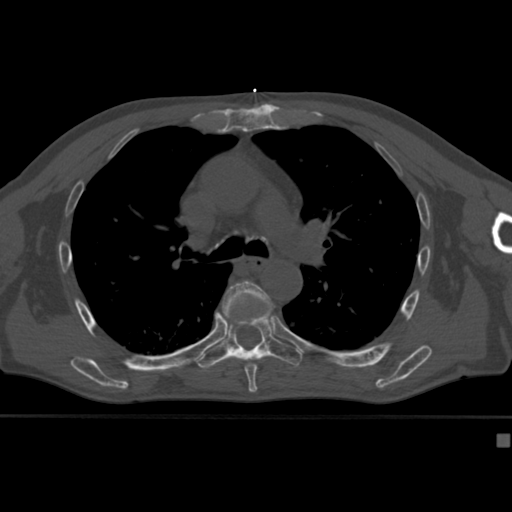
CT including the spine, one axial slice; slice 286 of 430 in the series (ordered by position); bone window (W 1800 / L 400 HU); 512 × 512 image matrix, field of view 337 × 337 mm. Male patient, age 64 years. From the clinical record (not read from this slice): primary cancer: uterus; vertebrae with lytic lesions (as recorded): T1, T4, T5, T7, L5.
Structures marked on this image (semi-automatically segmented with operator editing):
- T6 vertebra: bounding box (x1, y1, x2, y2) in pixels: (214, 280, 274, 382)
- T7 vertebra: (196, 312, 303, 373)